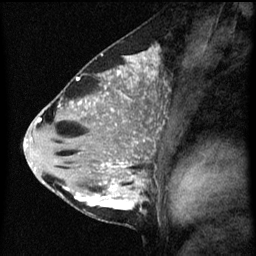
Breast MRI (dynamic contrast-enhanced), one sagittal slice; slice 30 of 60 in the series (ordered by position); dynamic contrast-enhanced series, image 2 of 3 at this slice position (ordered by acquisition); 1.5 T; TE 4.2 ms, TR 8 ms; 256 × 256 image matrix. Patient: female, 33 years.
Annotated regions visible in this slice (semi-automatically segmented with operator editing):
- analysis volume of interest (the breast-tissue region the enhancement analysis was run in; not a lesion): bounding box [x1, y1, x2, y2] px = [71, 118, 159, 215]
- tumour enhancement mask (voxels above the 70 % enhancement threshold inside the analysis volume of interest): [75, 162, 141, 211]